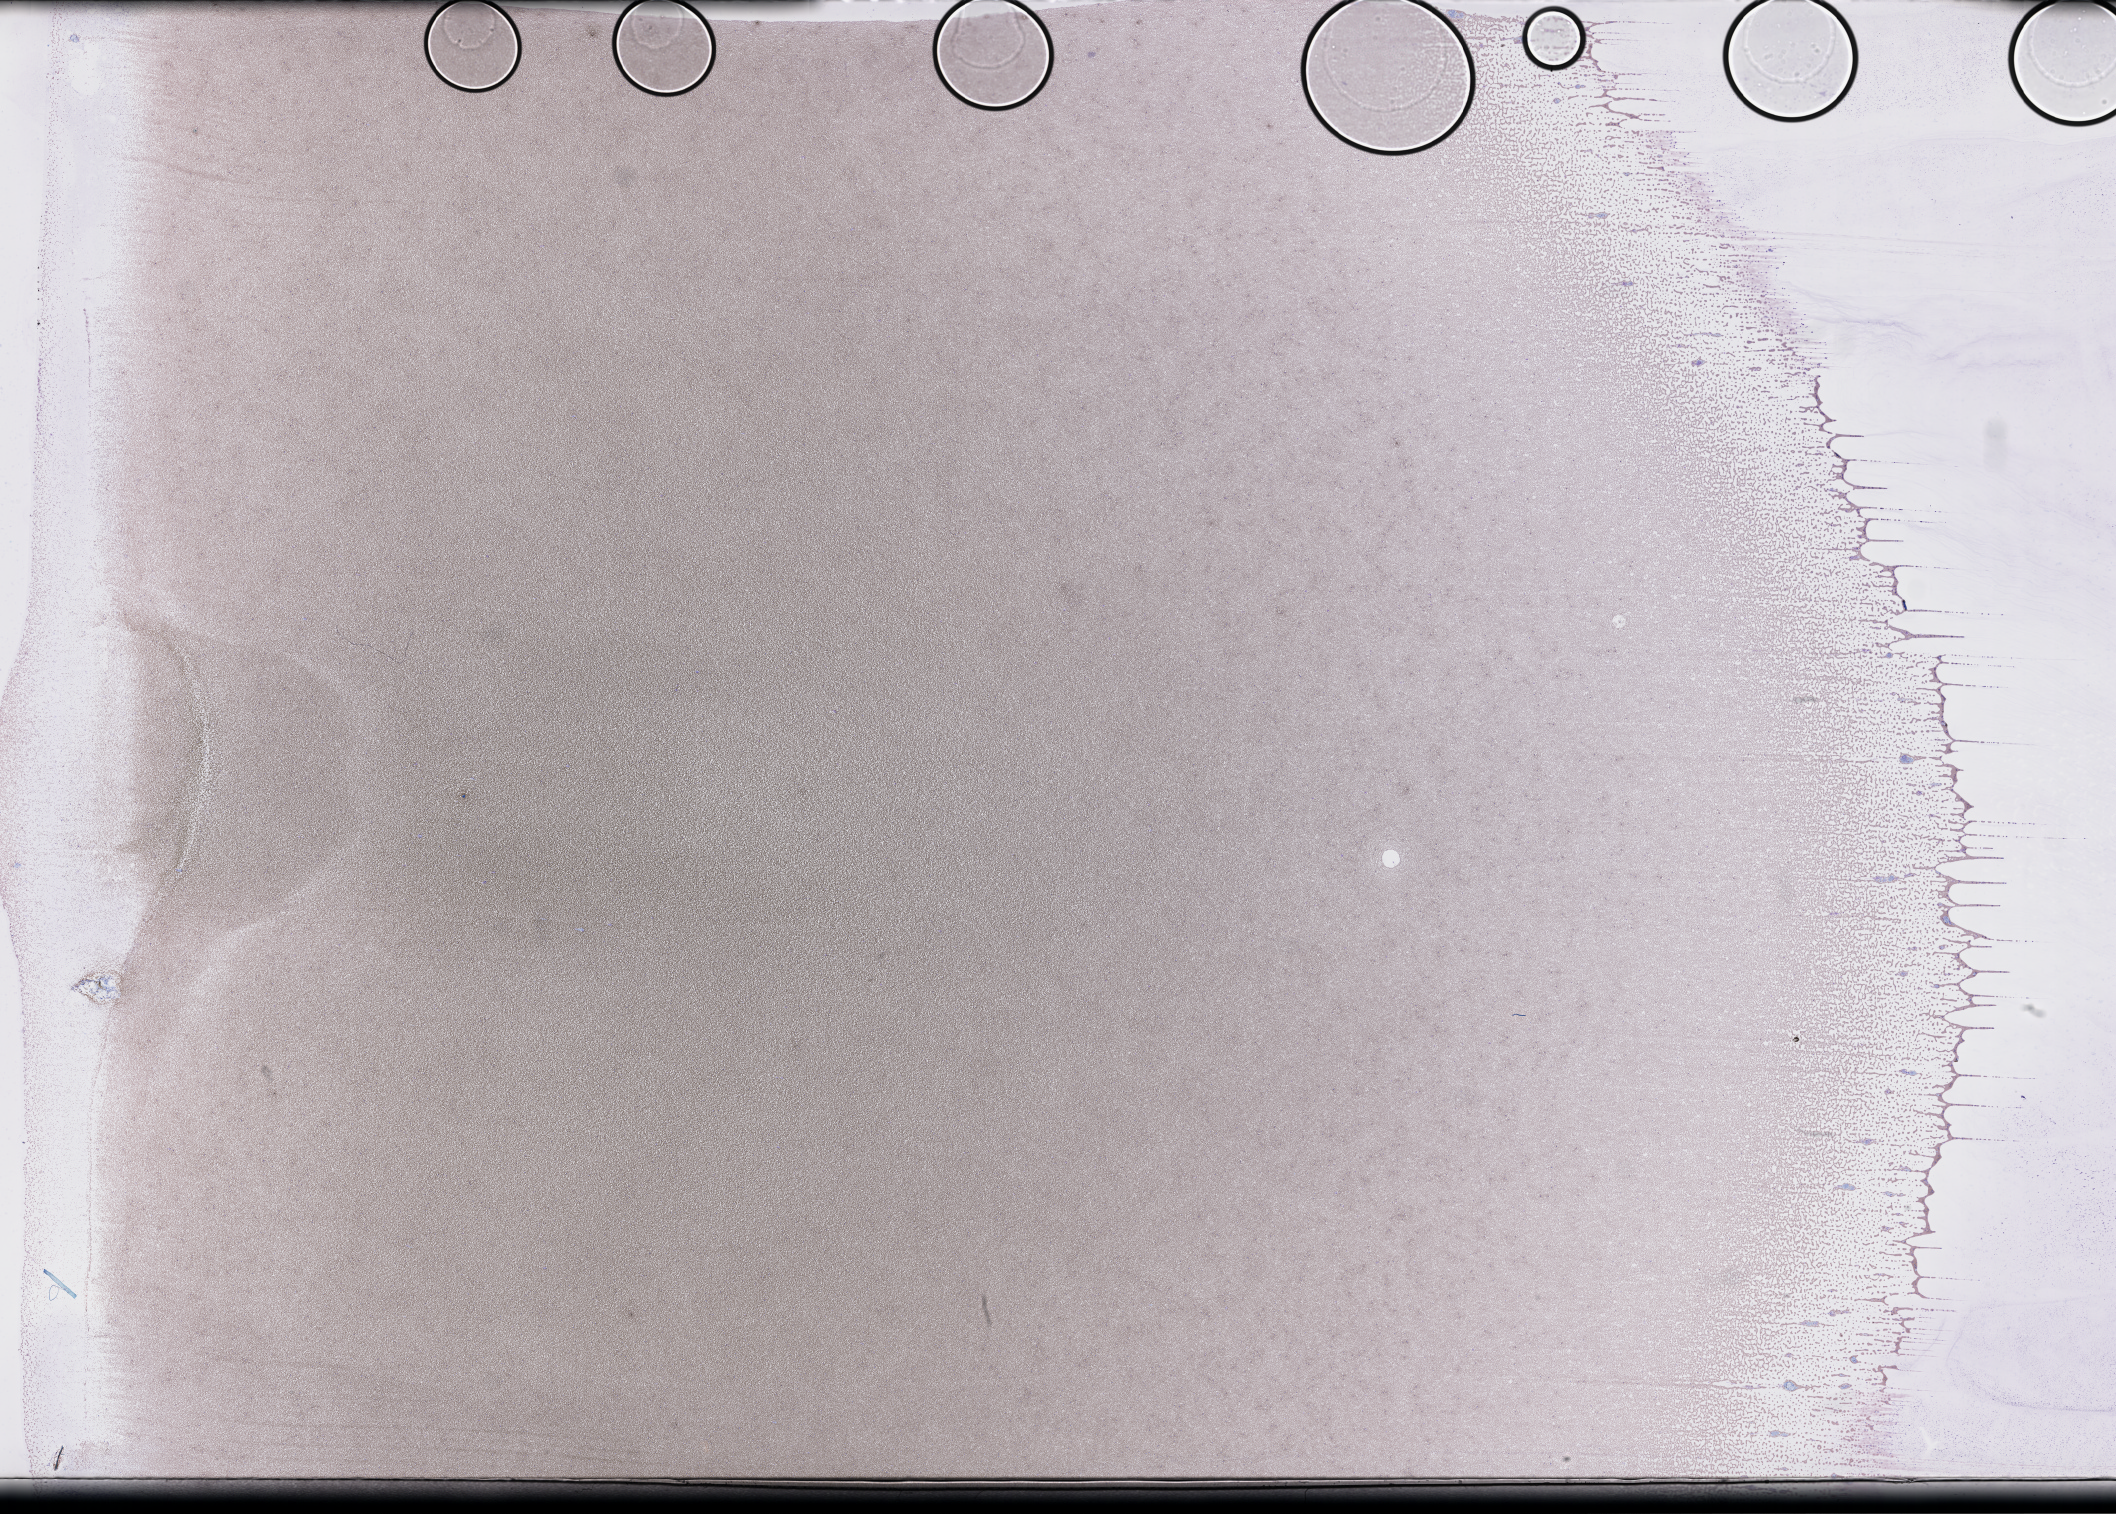
Whole-slide image of a whole blood smear, Wright–Giemsa stain, whole scanned area (about 34.2 x 24.5 mm) shown as a low-resolution overview; EDTA-anticoagulated smear. Patient: male.
• patient diagnosis: Plasma Cell Myeloma